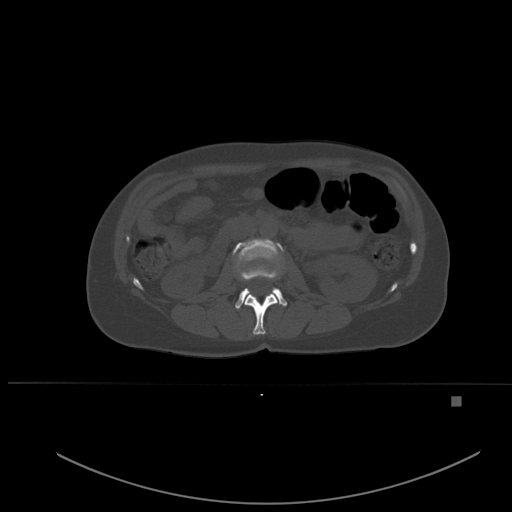
CT including the spine, one axial slice. Slice 223 of 651 in the series (ordered by position). Bone window (W 1800 / L 400 HU). 512 × 512 image matrix. Patient: female, 49 years. From the clinical record (not read from this slice): primary cancer: breast.
Outlined on this slice (semi-automatic segmentation, software-assisted and operator-edited):
- L1 vertebra: bounding box <244,293,278,335> (left, top, right, bottom; pixels)
- L2 vertebra: <233,239,287,309>